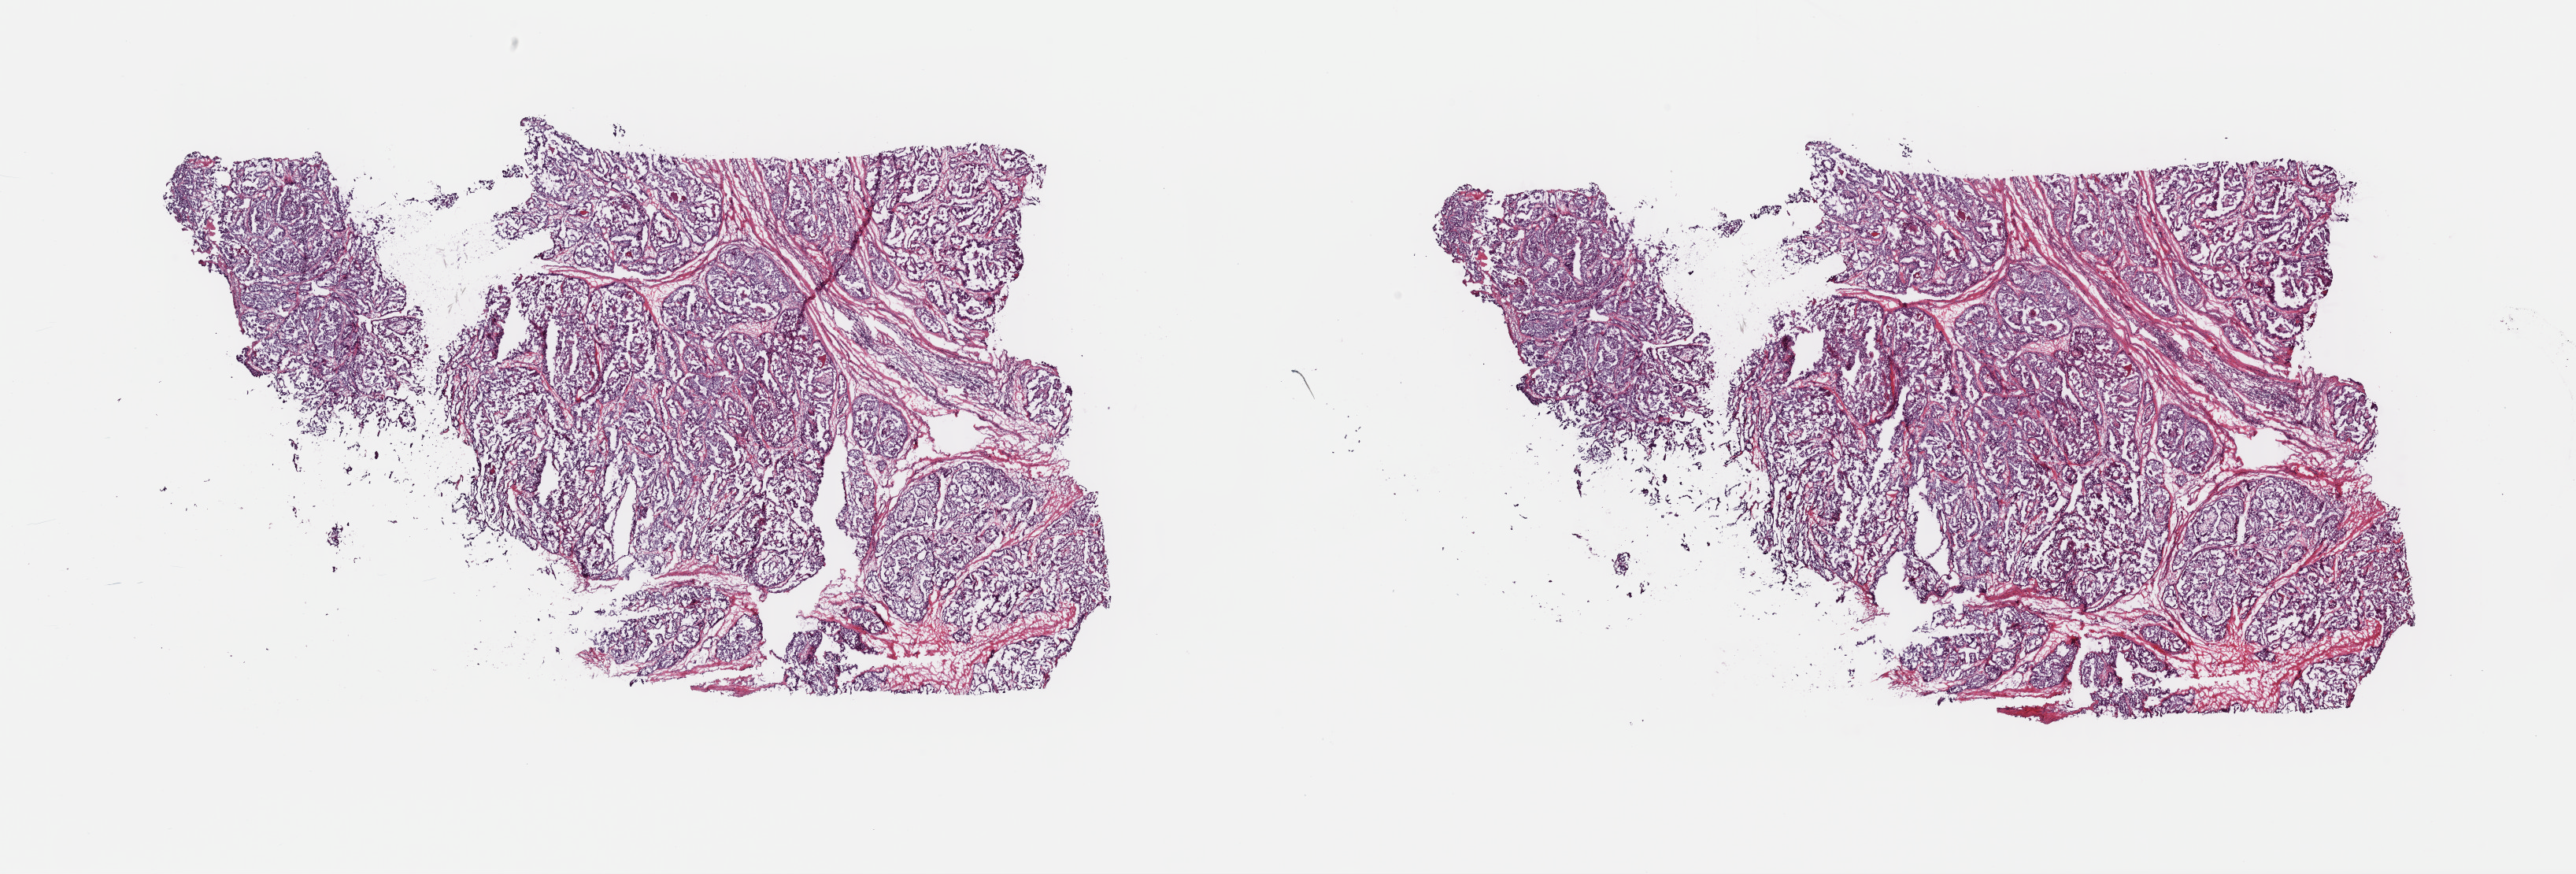
Whole-slide histology image, Hematoxylin and eosin (H&E) stained, shown as a low-resolution overview of the whole scanned area (about 25.8 x 8.8 mm), frozen section from the top of the tissue portion, primary tumour sample from the thyroid. Female, age 78 years at initial diagnosis. Slide review estimates, as recorded: tumour cells 85%, tumour nuclei 85%, normal cells 0%, stromal cells 15%, necrosis 0%. Inflammatory infiltration, as recorded: lymphocyte infiltration 0%, monocyte infiltration 0%, neutrophil infiltration 0%.
• TNM: T4a N1a M0
• pathologic diagnosis: Papillary adenocarcinoma, NOS (thyroid gland)
• AJCC pathologic stage: IVA (6th edition)
• lymph nodes positive (case pathology): 2 of 17 examined